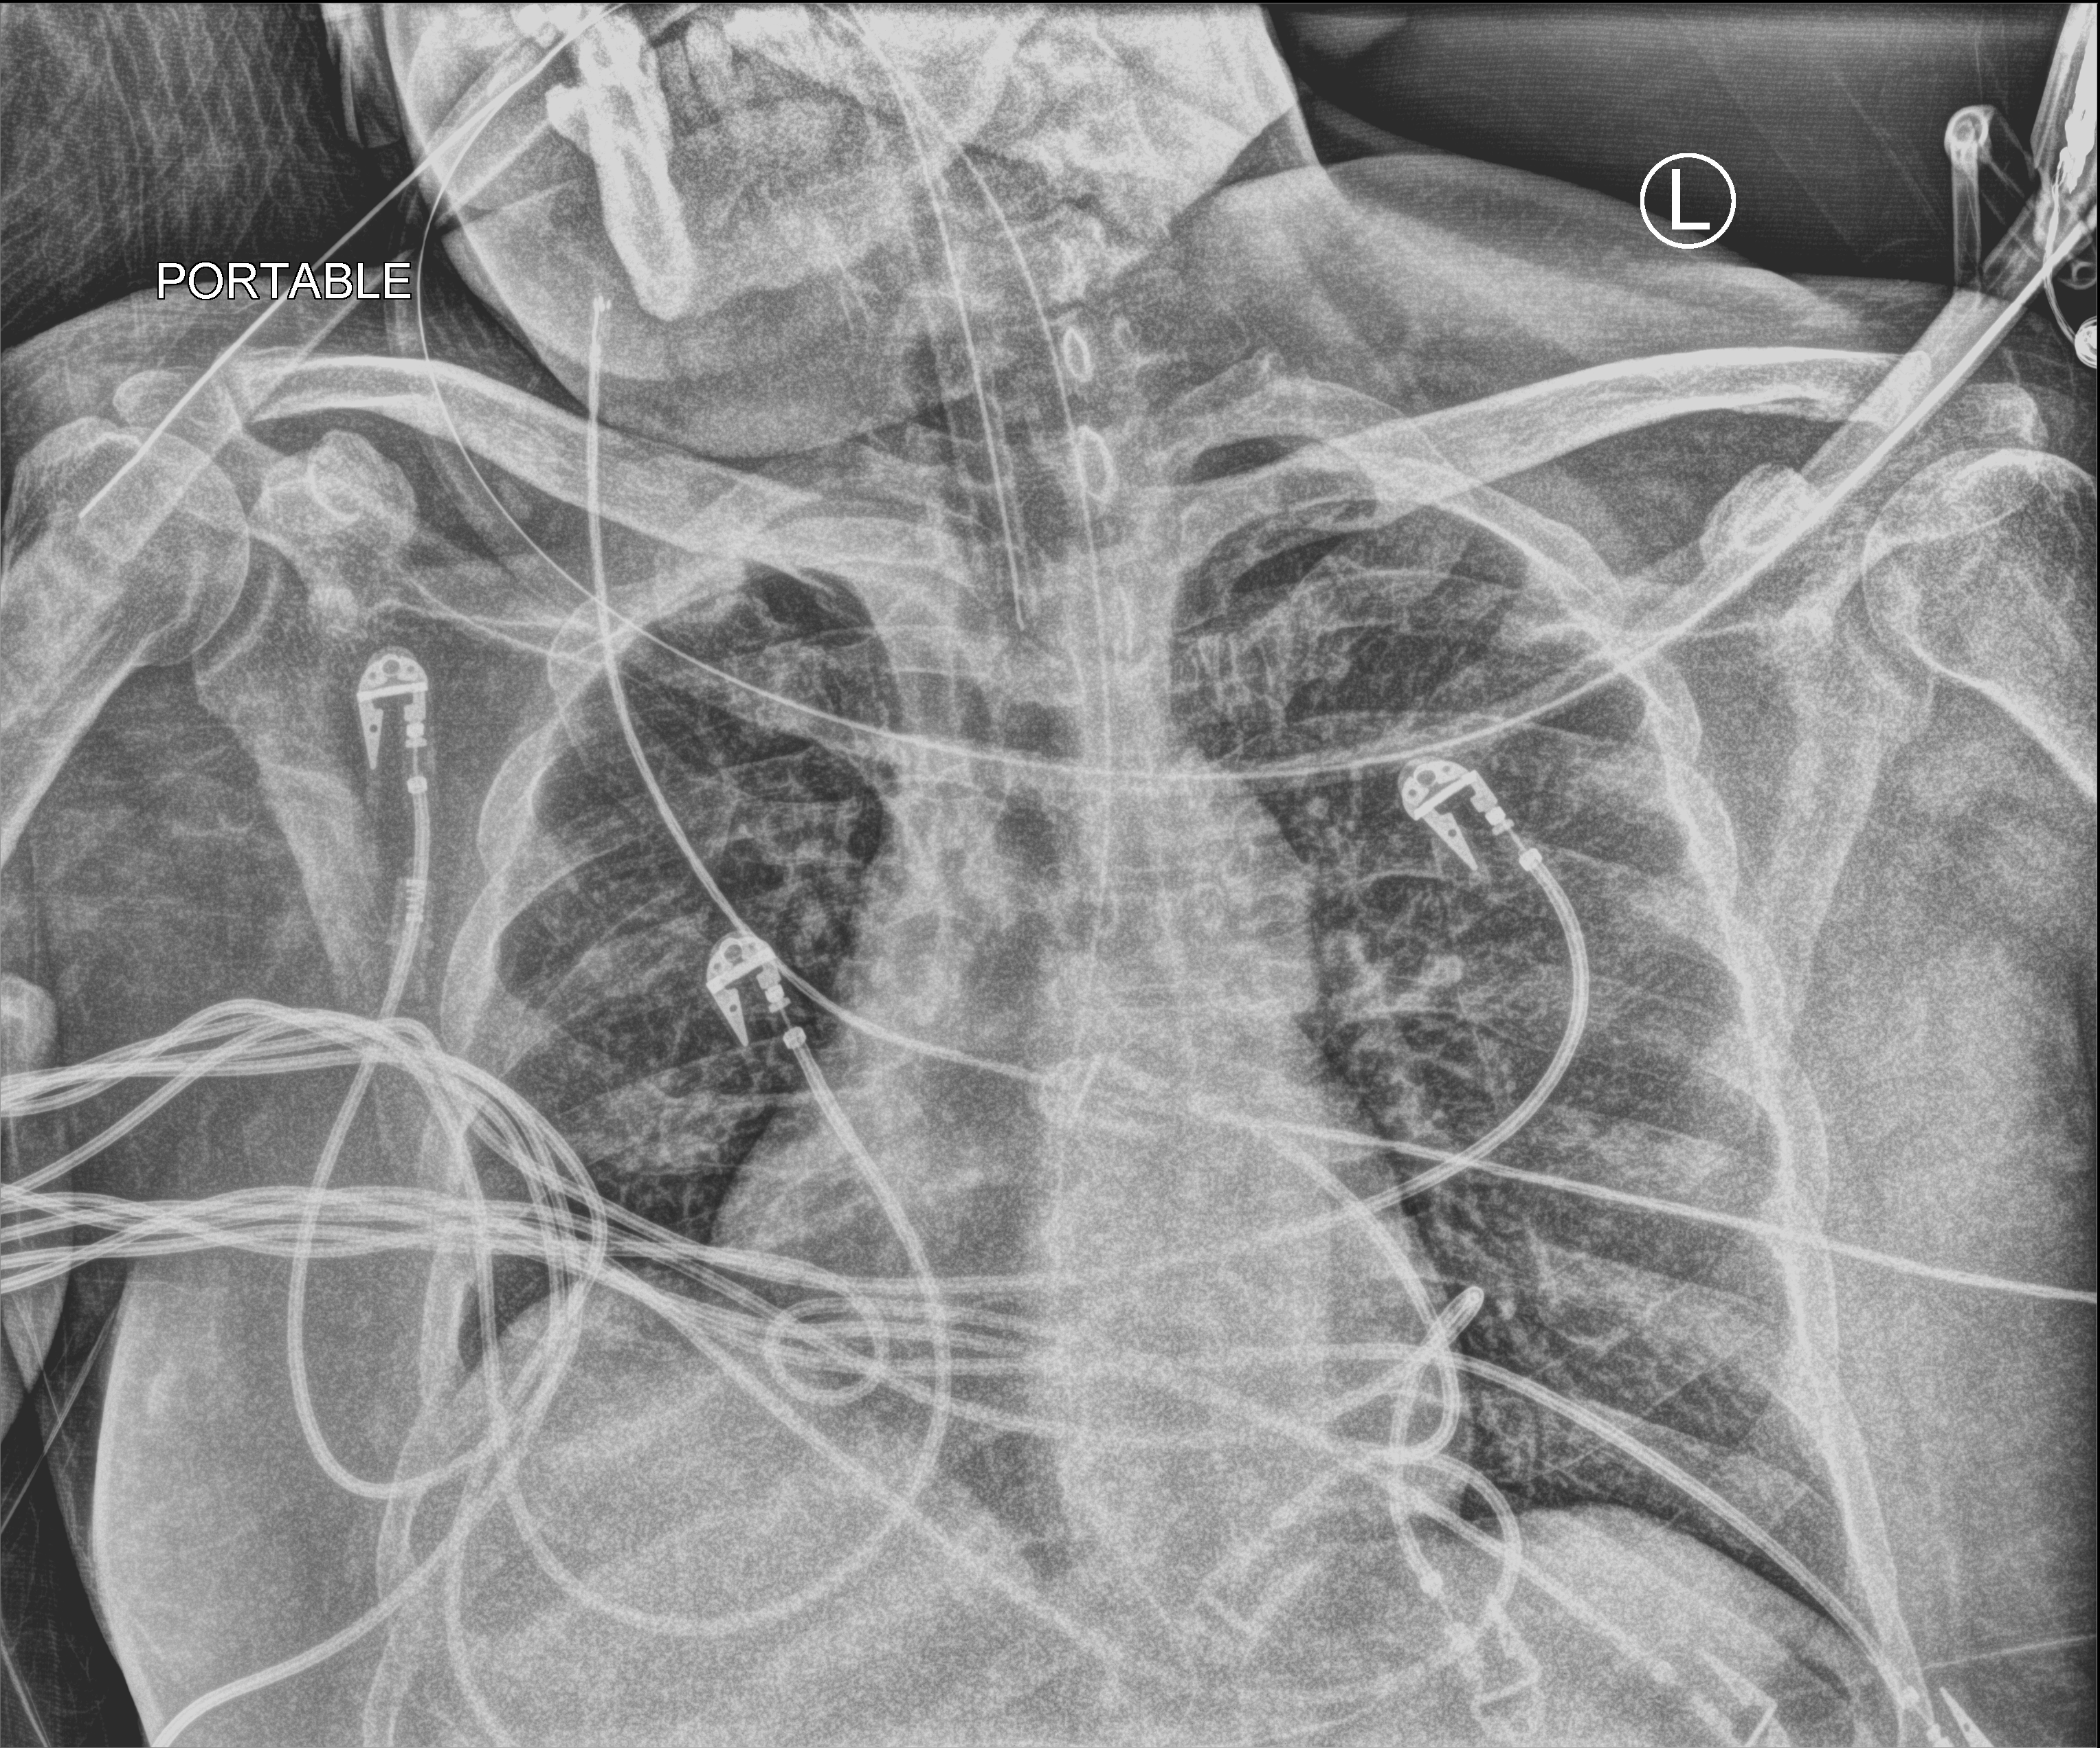
Portable chest radiograph, anteroposterior (AP) projection. Patient hospitalised with COVID-19, aged 18–59 years.
Admission-level facts for this patient (not findings on this image; timing relative to this image not recorded):
- length of hospital stay: 37 days
- mechanically ventilated during this hospital stay: yes
- admitted to intensive care during this hospital stay: yes